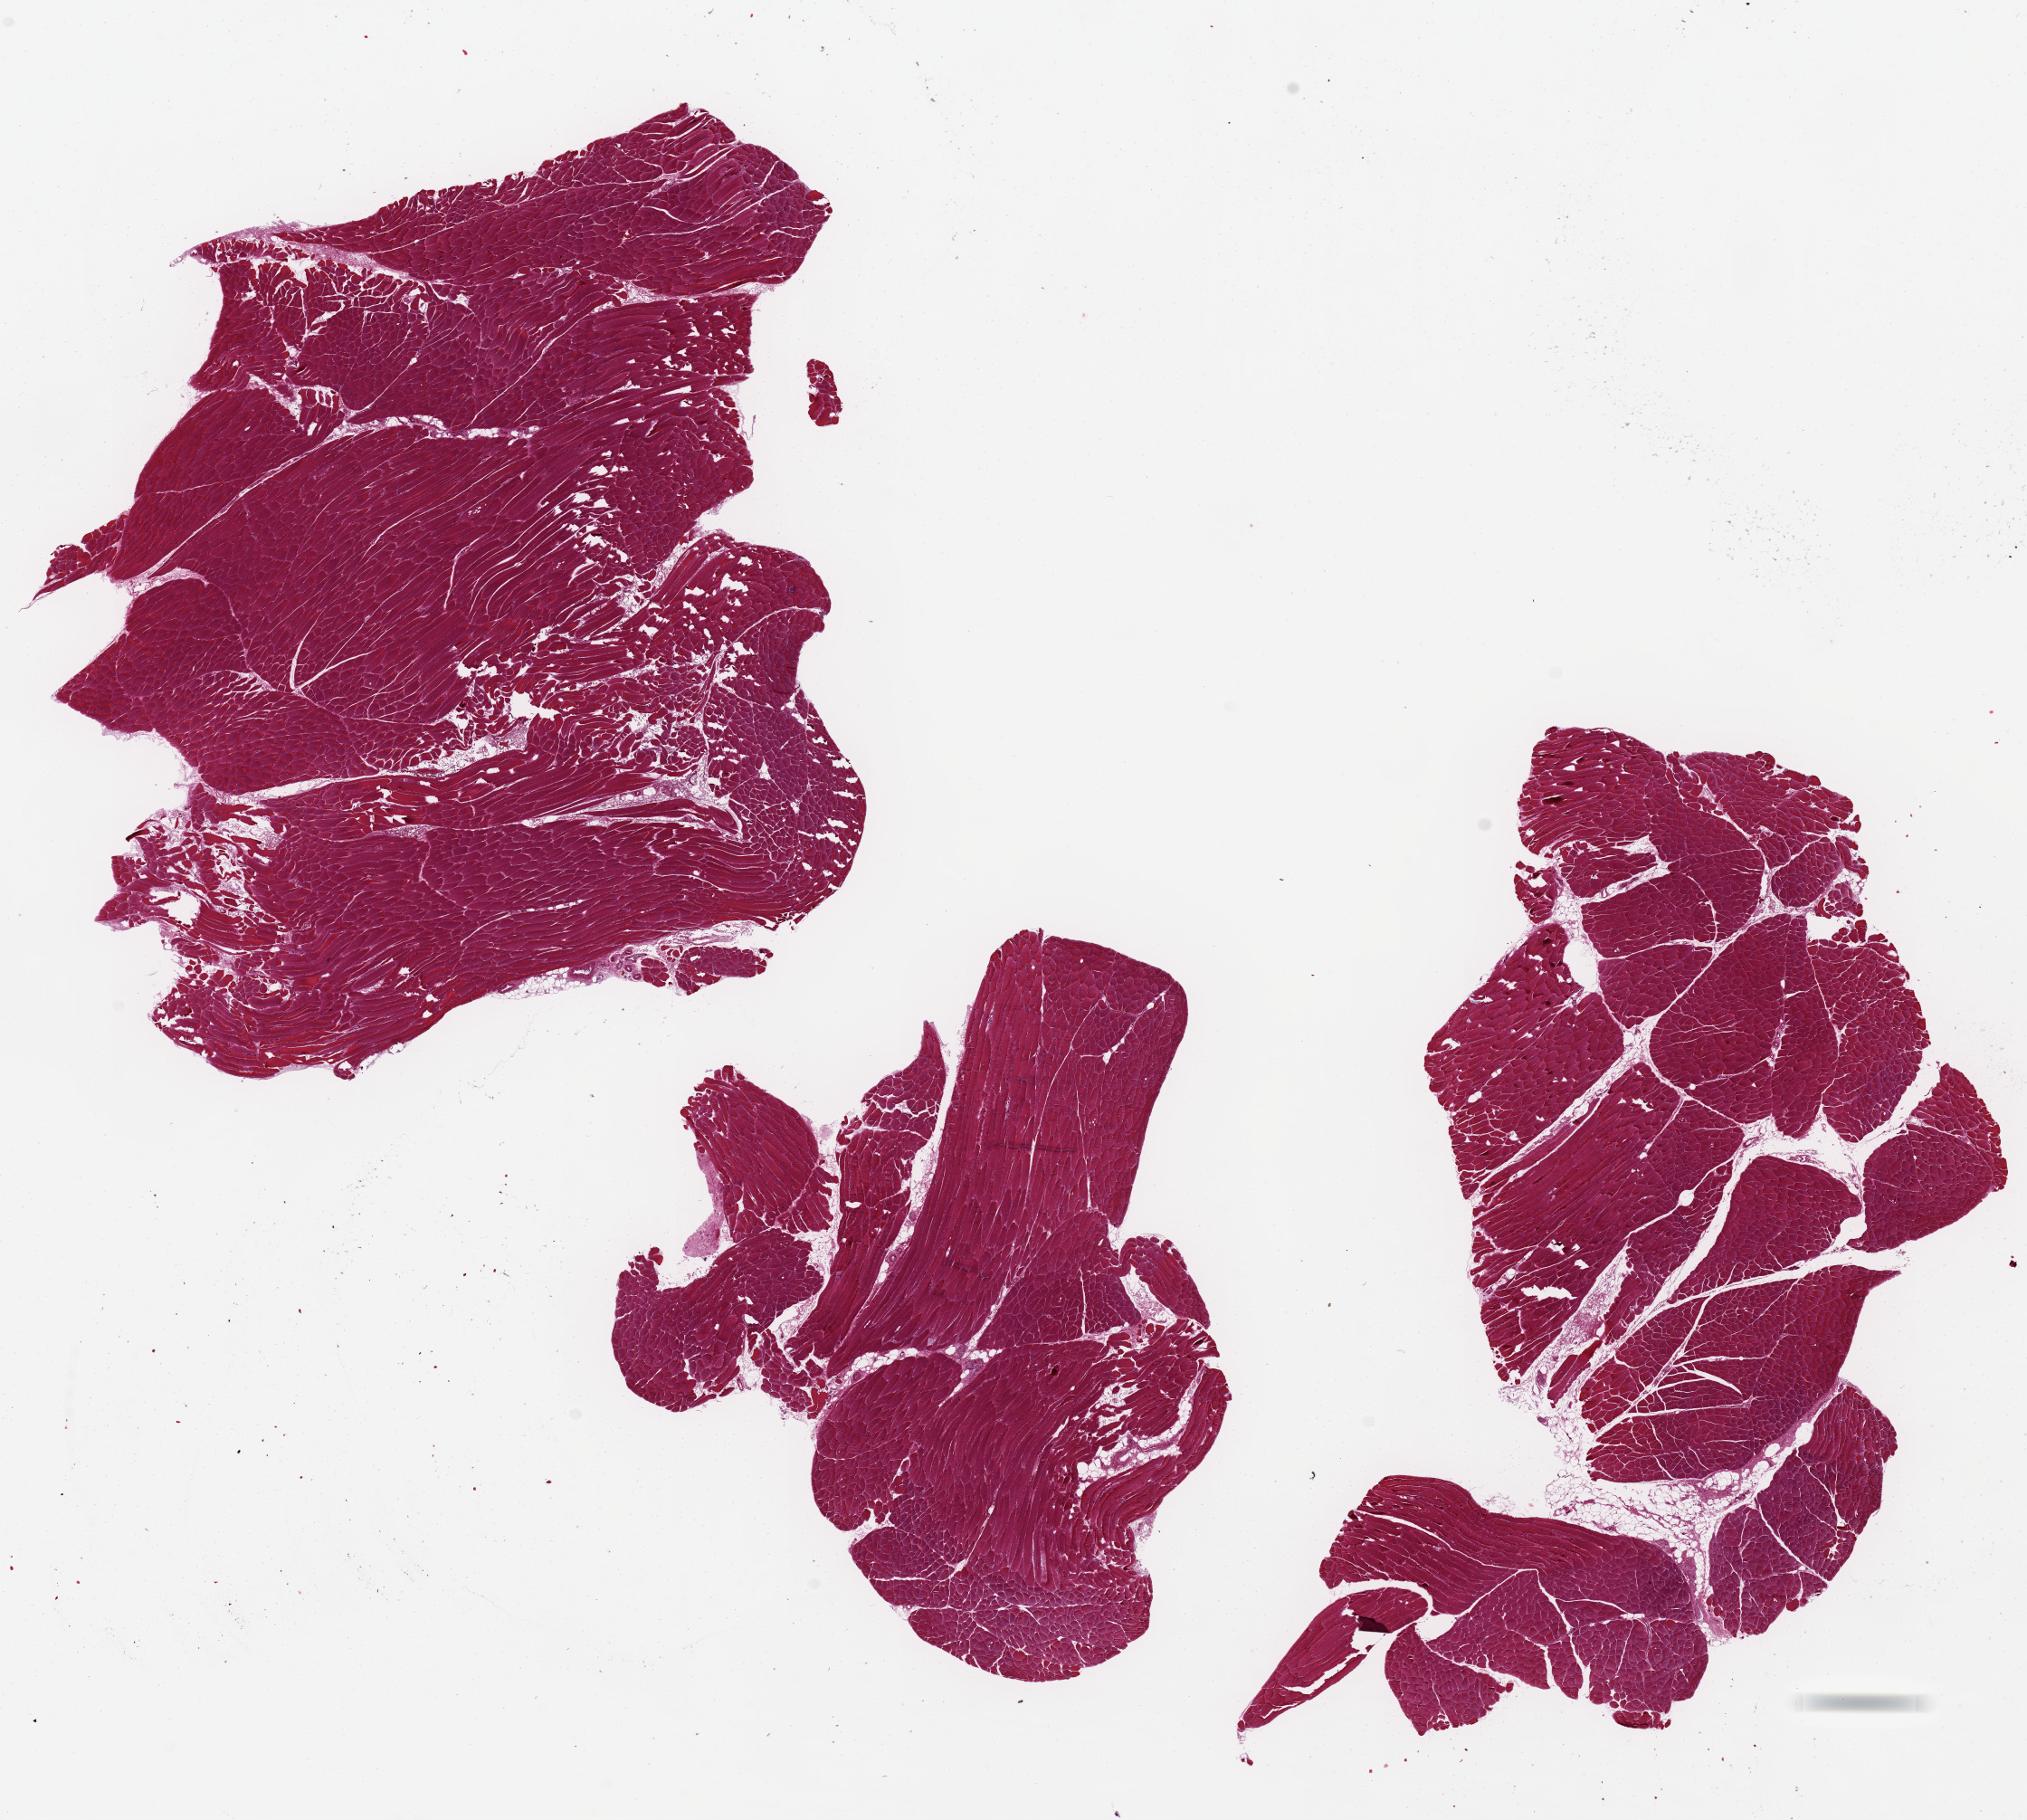
Digitized haematoxylin and eosin-stained section — shown as a low-resolution overview of the whole scanned area (about 17.7 x 15.9 mm). PAXgene-fixed paraffin-embedded (PFPE) section. Target tissue: skeletal muscle. Tissue donor sample. Female donor.
- pathologist's review note for this sample: 2 ~9x7mm aliquots, one fragmented. Poorly fixed